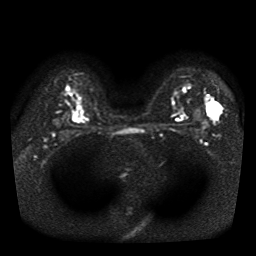
Breast MRI, one axial slice. Position 31 of 41 along the scan axis. Diffusion-weighted series; image 2 of 4 stored at this slice position (different b-values; order by instance number). 1.5 T. 5 mm slice thickness. 256 × 256 image matrix, field of view 330 × 330 mm. Female patient.
Annotated regions visible in this slice (outlined manually by an expert reader):
- tumour on diffusion-weighted imaging: bounding box <209,102,222,117> (left, top, right, bottom; pixels)